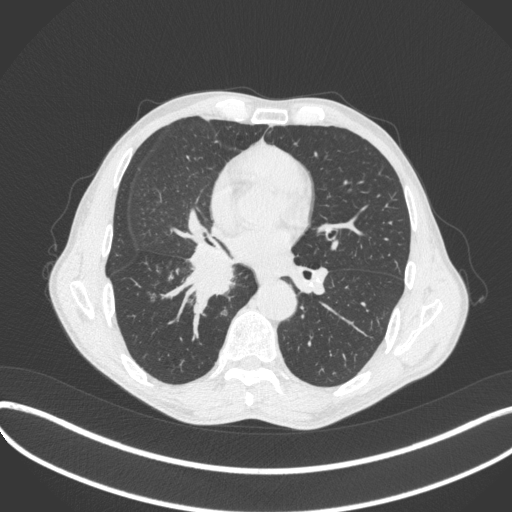
Chest CT, one axial slice. Reconstruction kernel B31f. 120 kVp. Lung window (W 1500 / L -600 HU). 512 × 512 image matrix, field of view 400 × 400 mm. Male patient, age 65 years. Case-level facts recorded for this patient, not image findings: clinical TNM (as recorded): T2a N0 M0; histopathological grade: G2.
Structures marked on this image (bounding box drawn by a radiologist):
- lung tumour (recorded histology: squamous cell carcinoma): bounding box (x1, y1, x2, y2) in pixels: (181, 240, 237, 303)